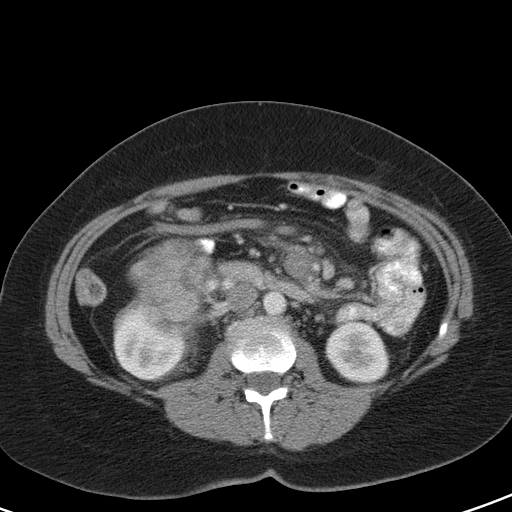
Contrast-enhanced abdominal CT, one axial slice; intravenous contrast given; soft-tissue window (W 400 / L 40 HU); 5 mm slice thickness; 512 × 512 image matrix, field of view 356 × 356 mm. Female patient, age 51 years. Case-level facts recorded for this patient, not image findings: diagnosis: adrenocortical carcinoma; tumour side: right adrenal; tumour size at pathology: 17 cm.
Annotated regions visible in this slice (semi-automatically segmented with operator editing):
- mass: bounding box [x1, y1, x2, y2] px = [142, 242, 215, 321]